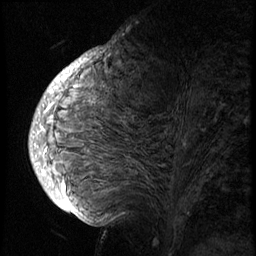
Breast MRI (dynamic contrast-enhanced), one sagittal slice; 3 images stored at this slice position (order not interpretable as contrast timing); 1.5 T; TE 4.2 ms, TR 8.9 ms; 256 × 256 image matrix. Female patient, age 57 years. Case-level facts recorded for this patient, not image findings: setting: breast cancer imaged before/during neoadjuvant chemotherapy; receptor status: HER2-positive.
Structures marked on this image (semi-automatic segmentation, software-assisted and operator-edited):
- analysis volume of interest (the breast-tissue region the enhancement analysis was run in; not a lesion): bounding box [x1, y1, x2, y2] px = [40, 62, 234, 175]
- tumour enhancement mask (voxels above the 140 % enhancement threshold inside the analysis volume of interest): [41, 65, 81, 173]